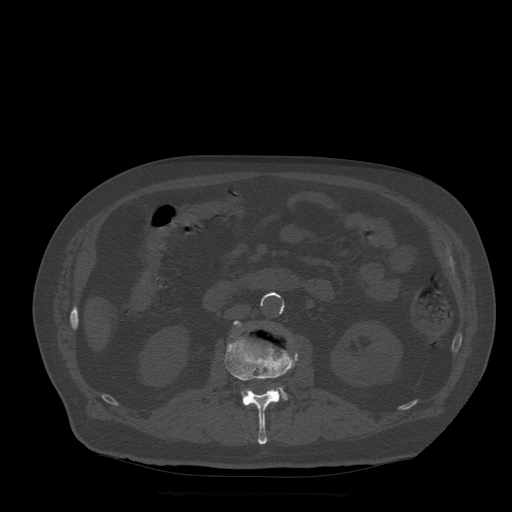
CT including the spine, one axial slice. Position 162 of 522 along the scan axis. Bone window (W 1800 / L 400 HU). 1.25 mm slice thickness. 512 × 512 image matrix. Patient age 72 years. From the clinical record (not read from this slice): primary cancer: prostate.
Annotated regions visible in this slice (semi-automatically segmented with operator editing):
- L2 vertebra: bounding box [x1, y1, x2, y2] px = [225, 337, 298, 445]
- L3 vertebra: [234, 321, 288, 401]